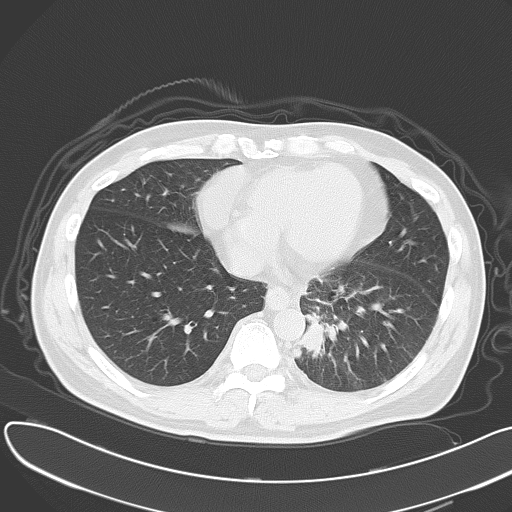
Chest CT, one axial slice; slice 17 of 55 in the series (ordered by position); reconstruction kernel B70f; lung window (W 1500 / L -600 HU); 5 mm slice thickness; 512 × 512 image matrix, field of view 376 × 376 mm. Patient: male, 55 years. Case-level facts recorded for this patient, not image findings: clinical TNM (as recorded): T2 N3 M0.
Structures marked on this image (rectangle marked by the reading radiologist):
- lung tumour (recorded histology: small cell carcinoma): box from (x=299, y=318) to (x=328, y=360) px